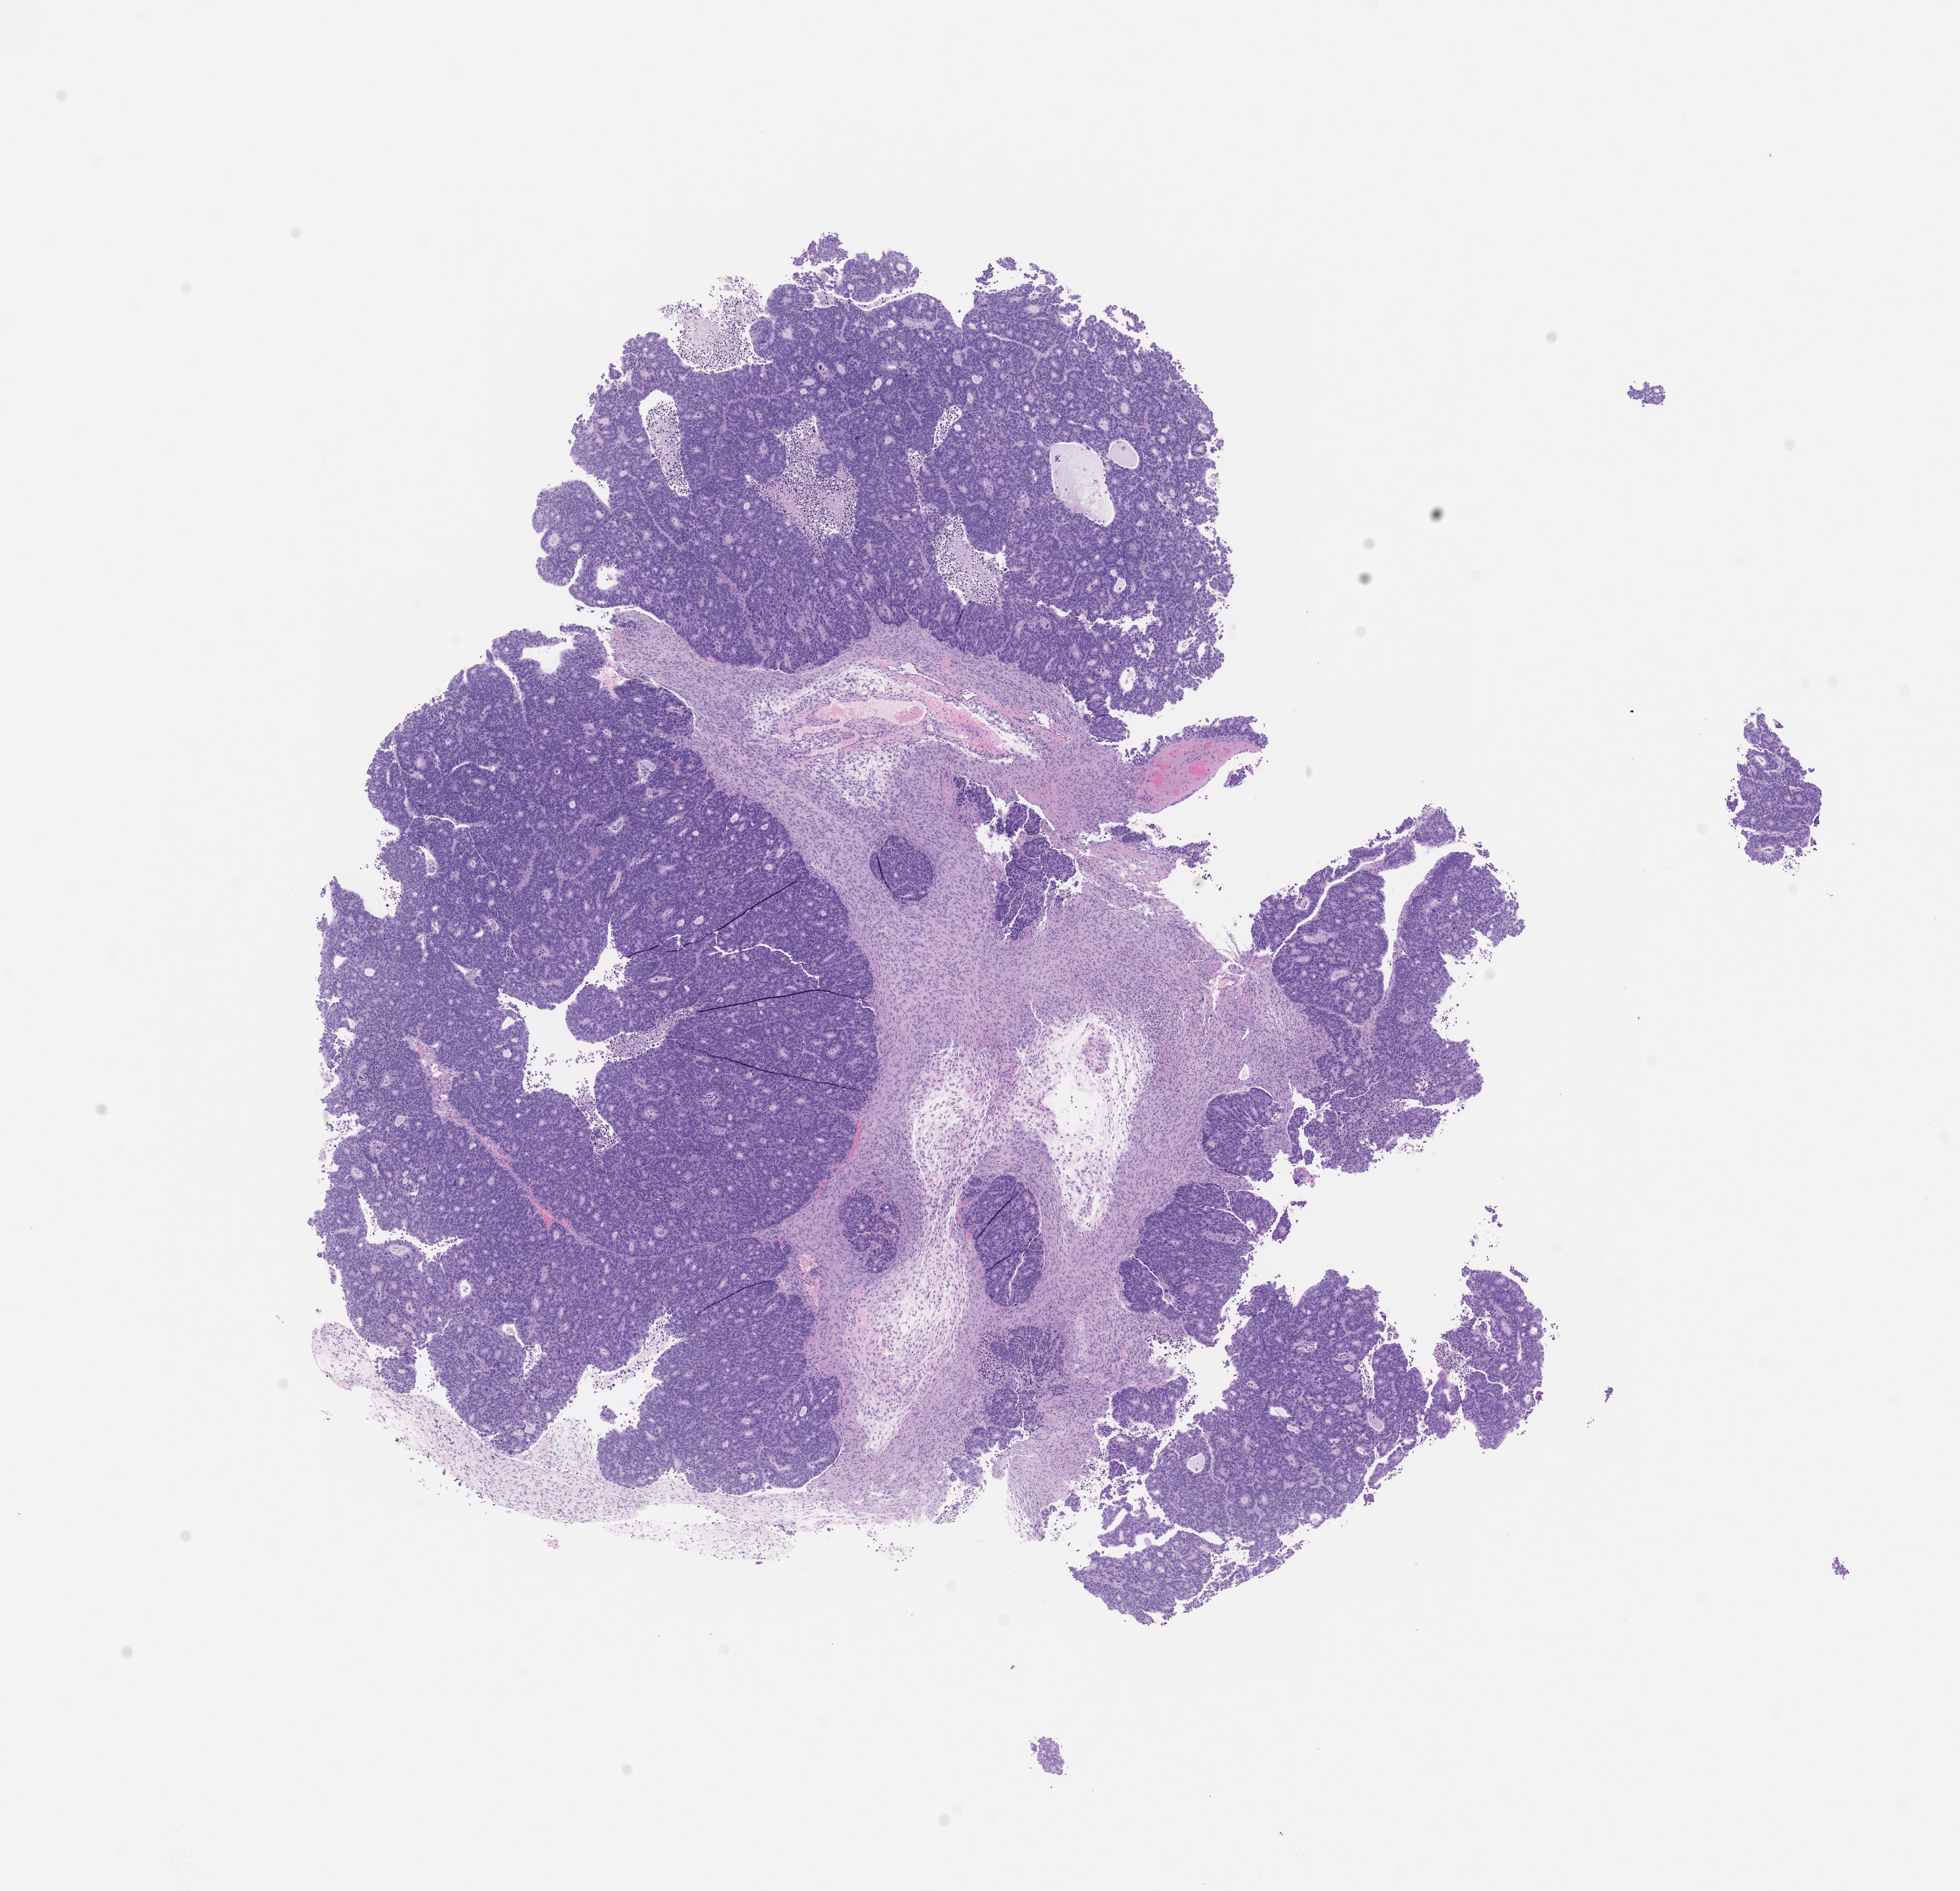
H&E whole-slide image of a patient-derived xenograft (PDX) tumor grown in a mouse, passage 0, low-resolution overview of the scanned area, about 12.0 x 11.6 mm; formalin-fixed, paraffin-embedded (FFPE) tissue; originating tumor site category: colon.
Originating patient diagnosis: Colon Adenocarcinoma.